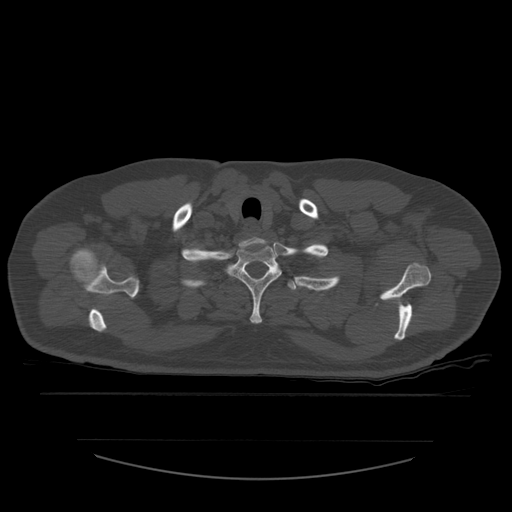
CT including the spine, one axial slice. Slice 467 of 532 in the series (ordered by position). 120 kVp. Bone window (W 1800 / L 400 HU). 1.25 mm slice thickness. 512 × 512 image matrix, field of view 441 × 441 mm. Patient age 44 years. Case-level facts recorded for this patient, not image findings: primary cancer: soft tissue sarcoma.
Annotated regions visible in this slice (semi-automatic segmentation, software-assisted and operator-edited):
- T1 vertebra: bounding box <227,241,282,324> (left, top, right, bottom; pixels)
- T2 vertebra: <288,280,313,291>